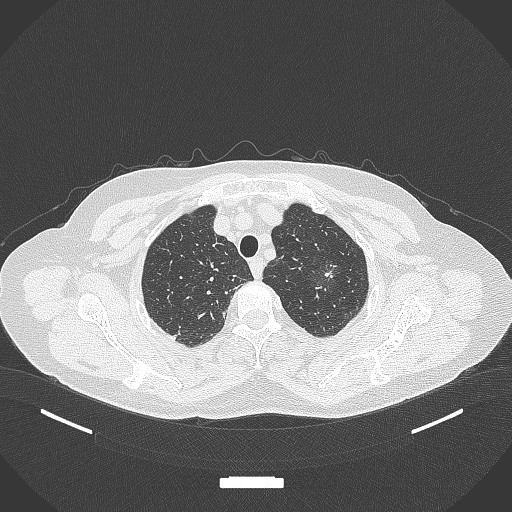
Chest CT, one axial slice. Position 305 of 369 along the scan axis. 120 kVp. Lung window (W 1500 / L -600 HU). 1 mm slice thickness. 512 × 512 image matrix, field of view 400 × 400 mm. Patient: female, 64 years. Case-level facts recorded for this patient, not image findings: clinical TNM (as recorded): T1c N0 M0.
Annotated regions visible in this slice (bounding box drawn by a radiologist):
- lung tumour (recorded histology: adenocarcinoma): bounding box <305,250,344,291> (left, top, right, bottom; pixels)